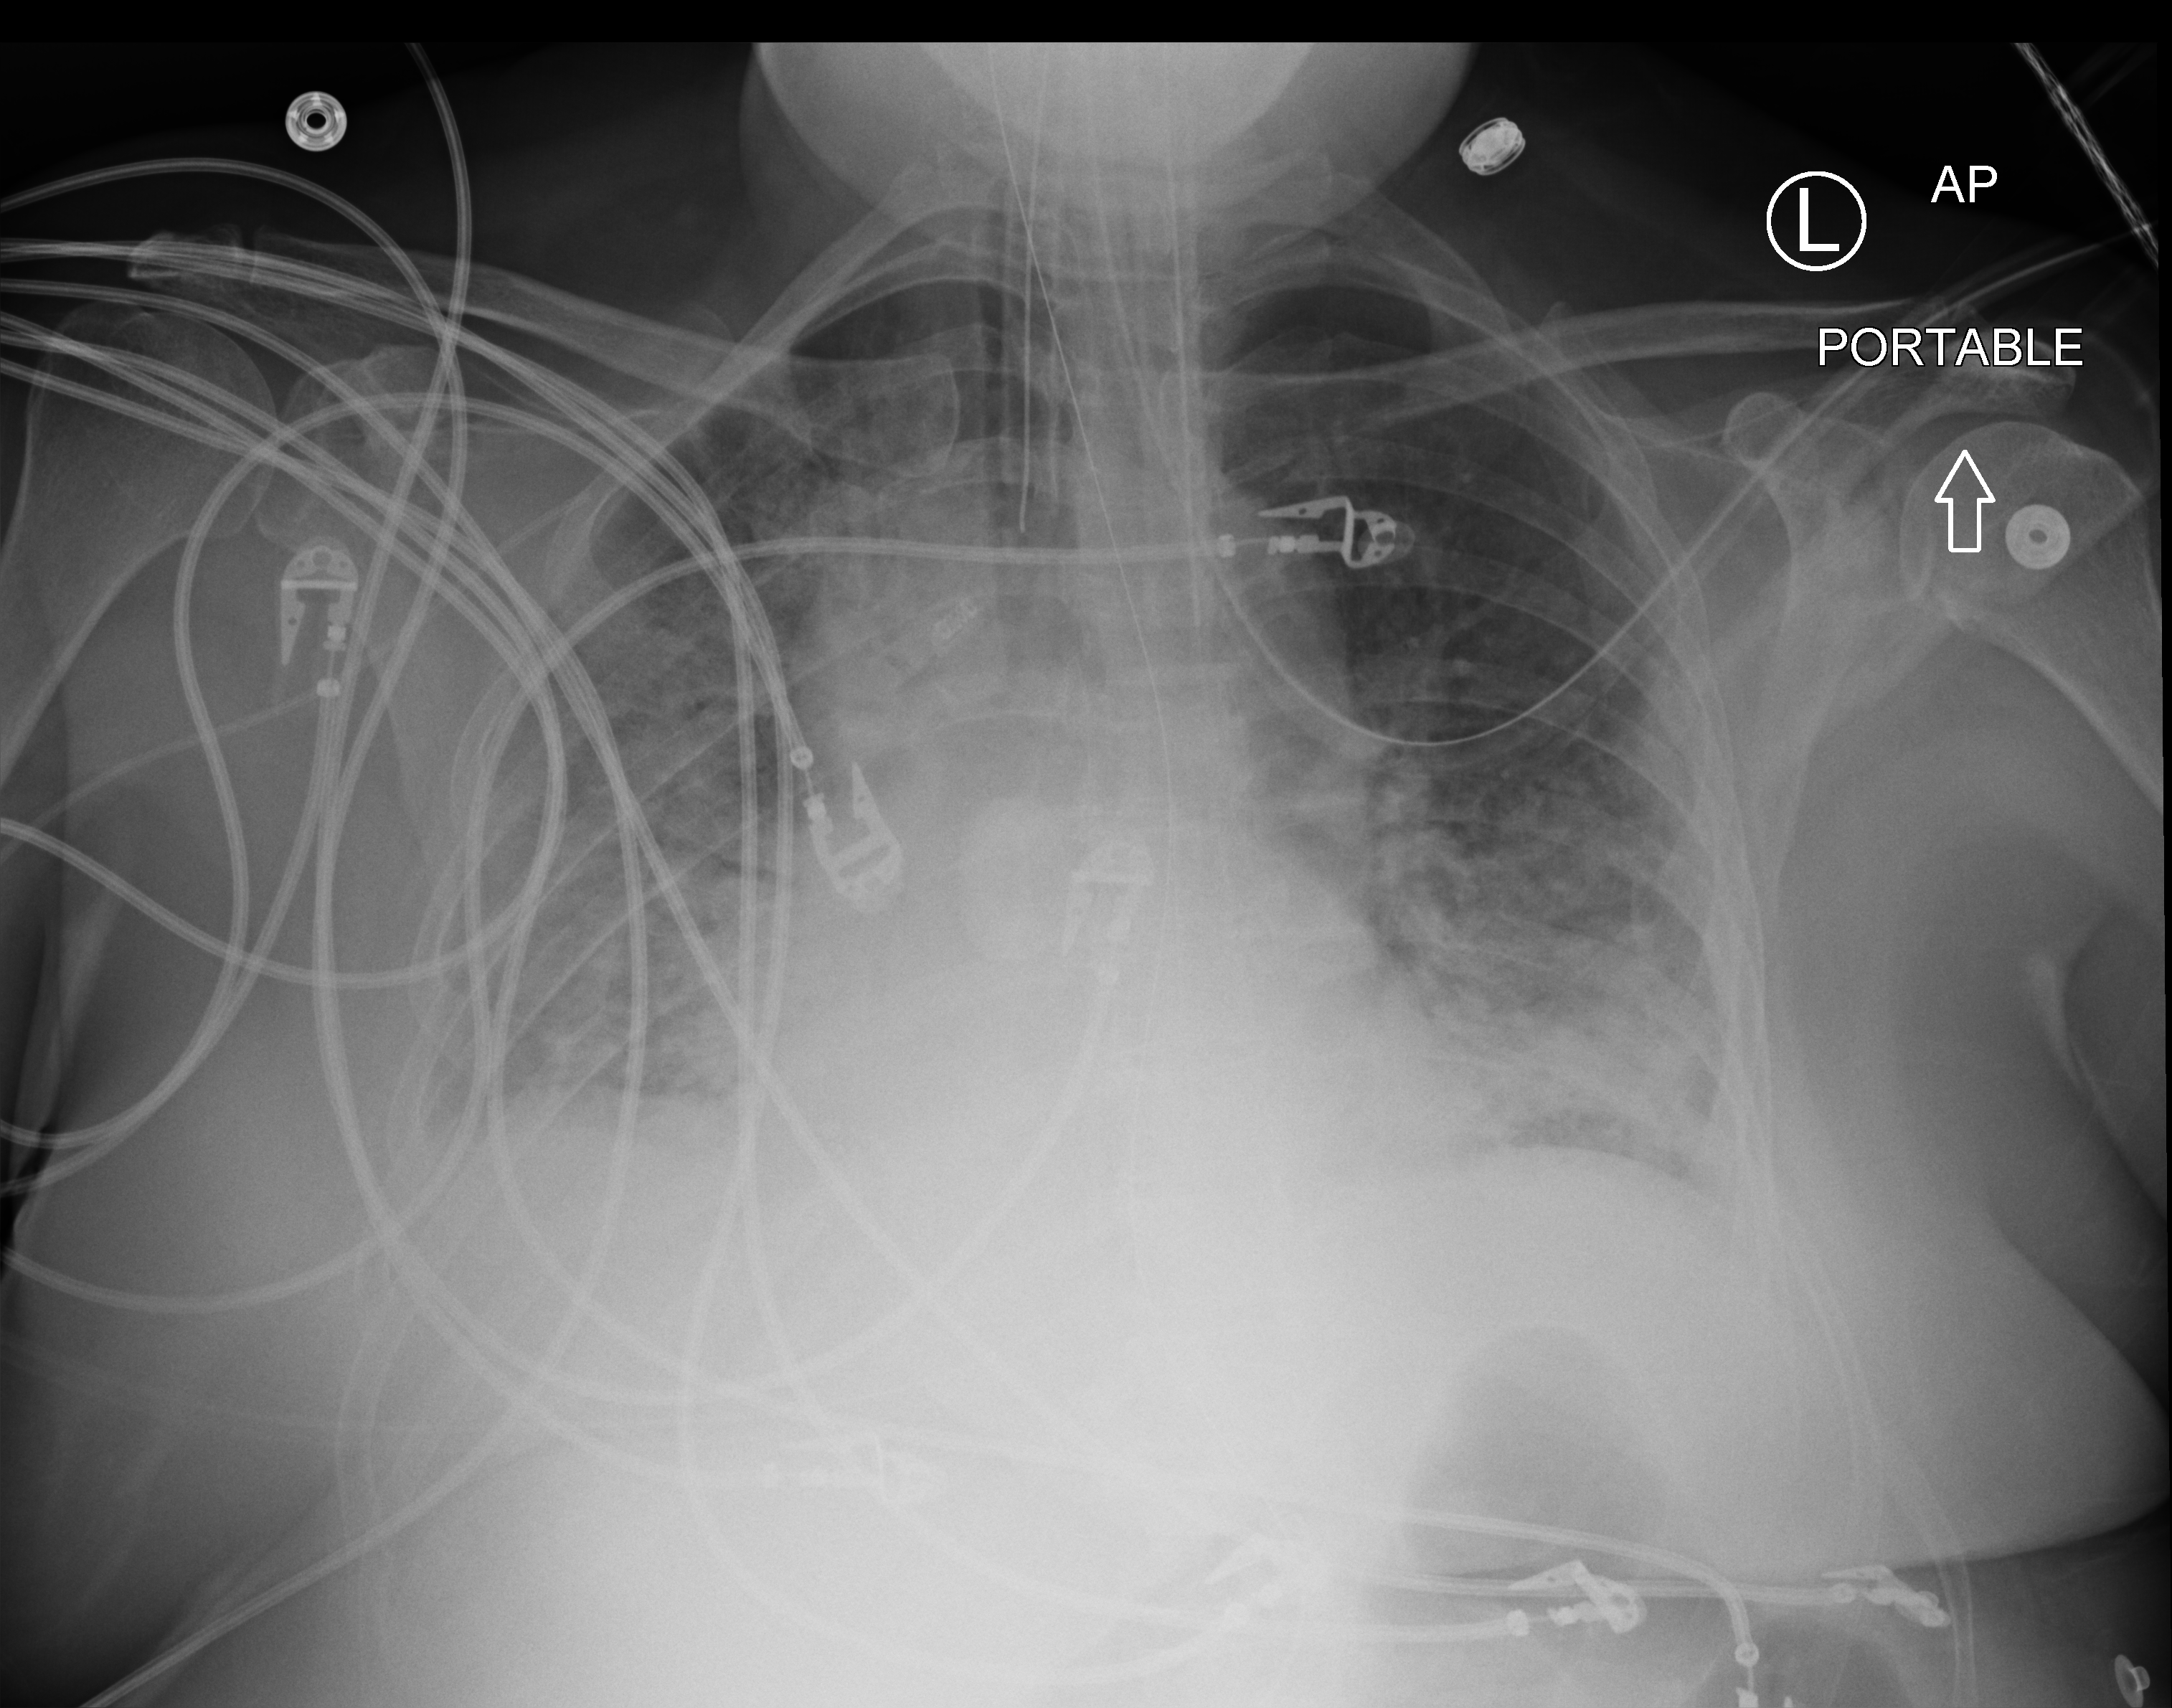
Bedside chest radiograph (computed radiography); anteroposterior (AP) projection. Female patient hospitalised with COVID-19, age 18–59 years.
Admission-level facts for this patient (not findings on this image; timing relative to this image not recorded): other chronic lung disease (admission record): no.